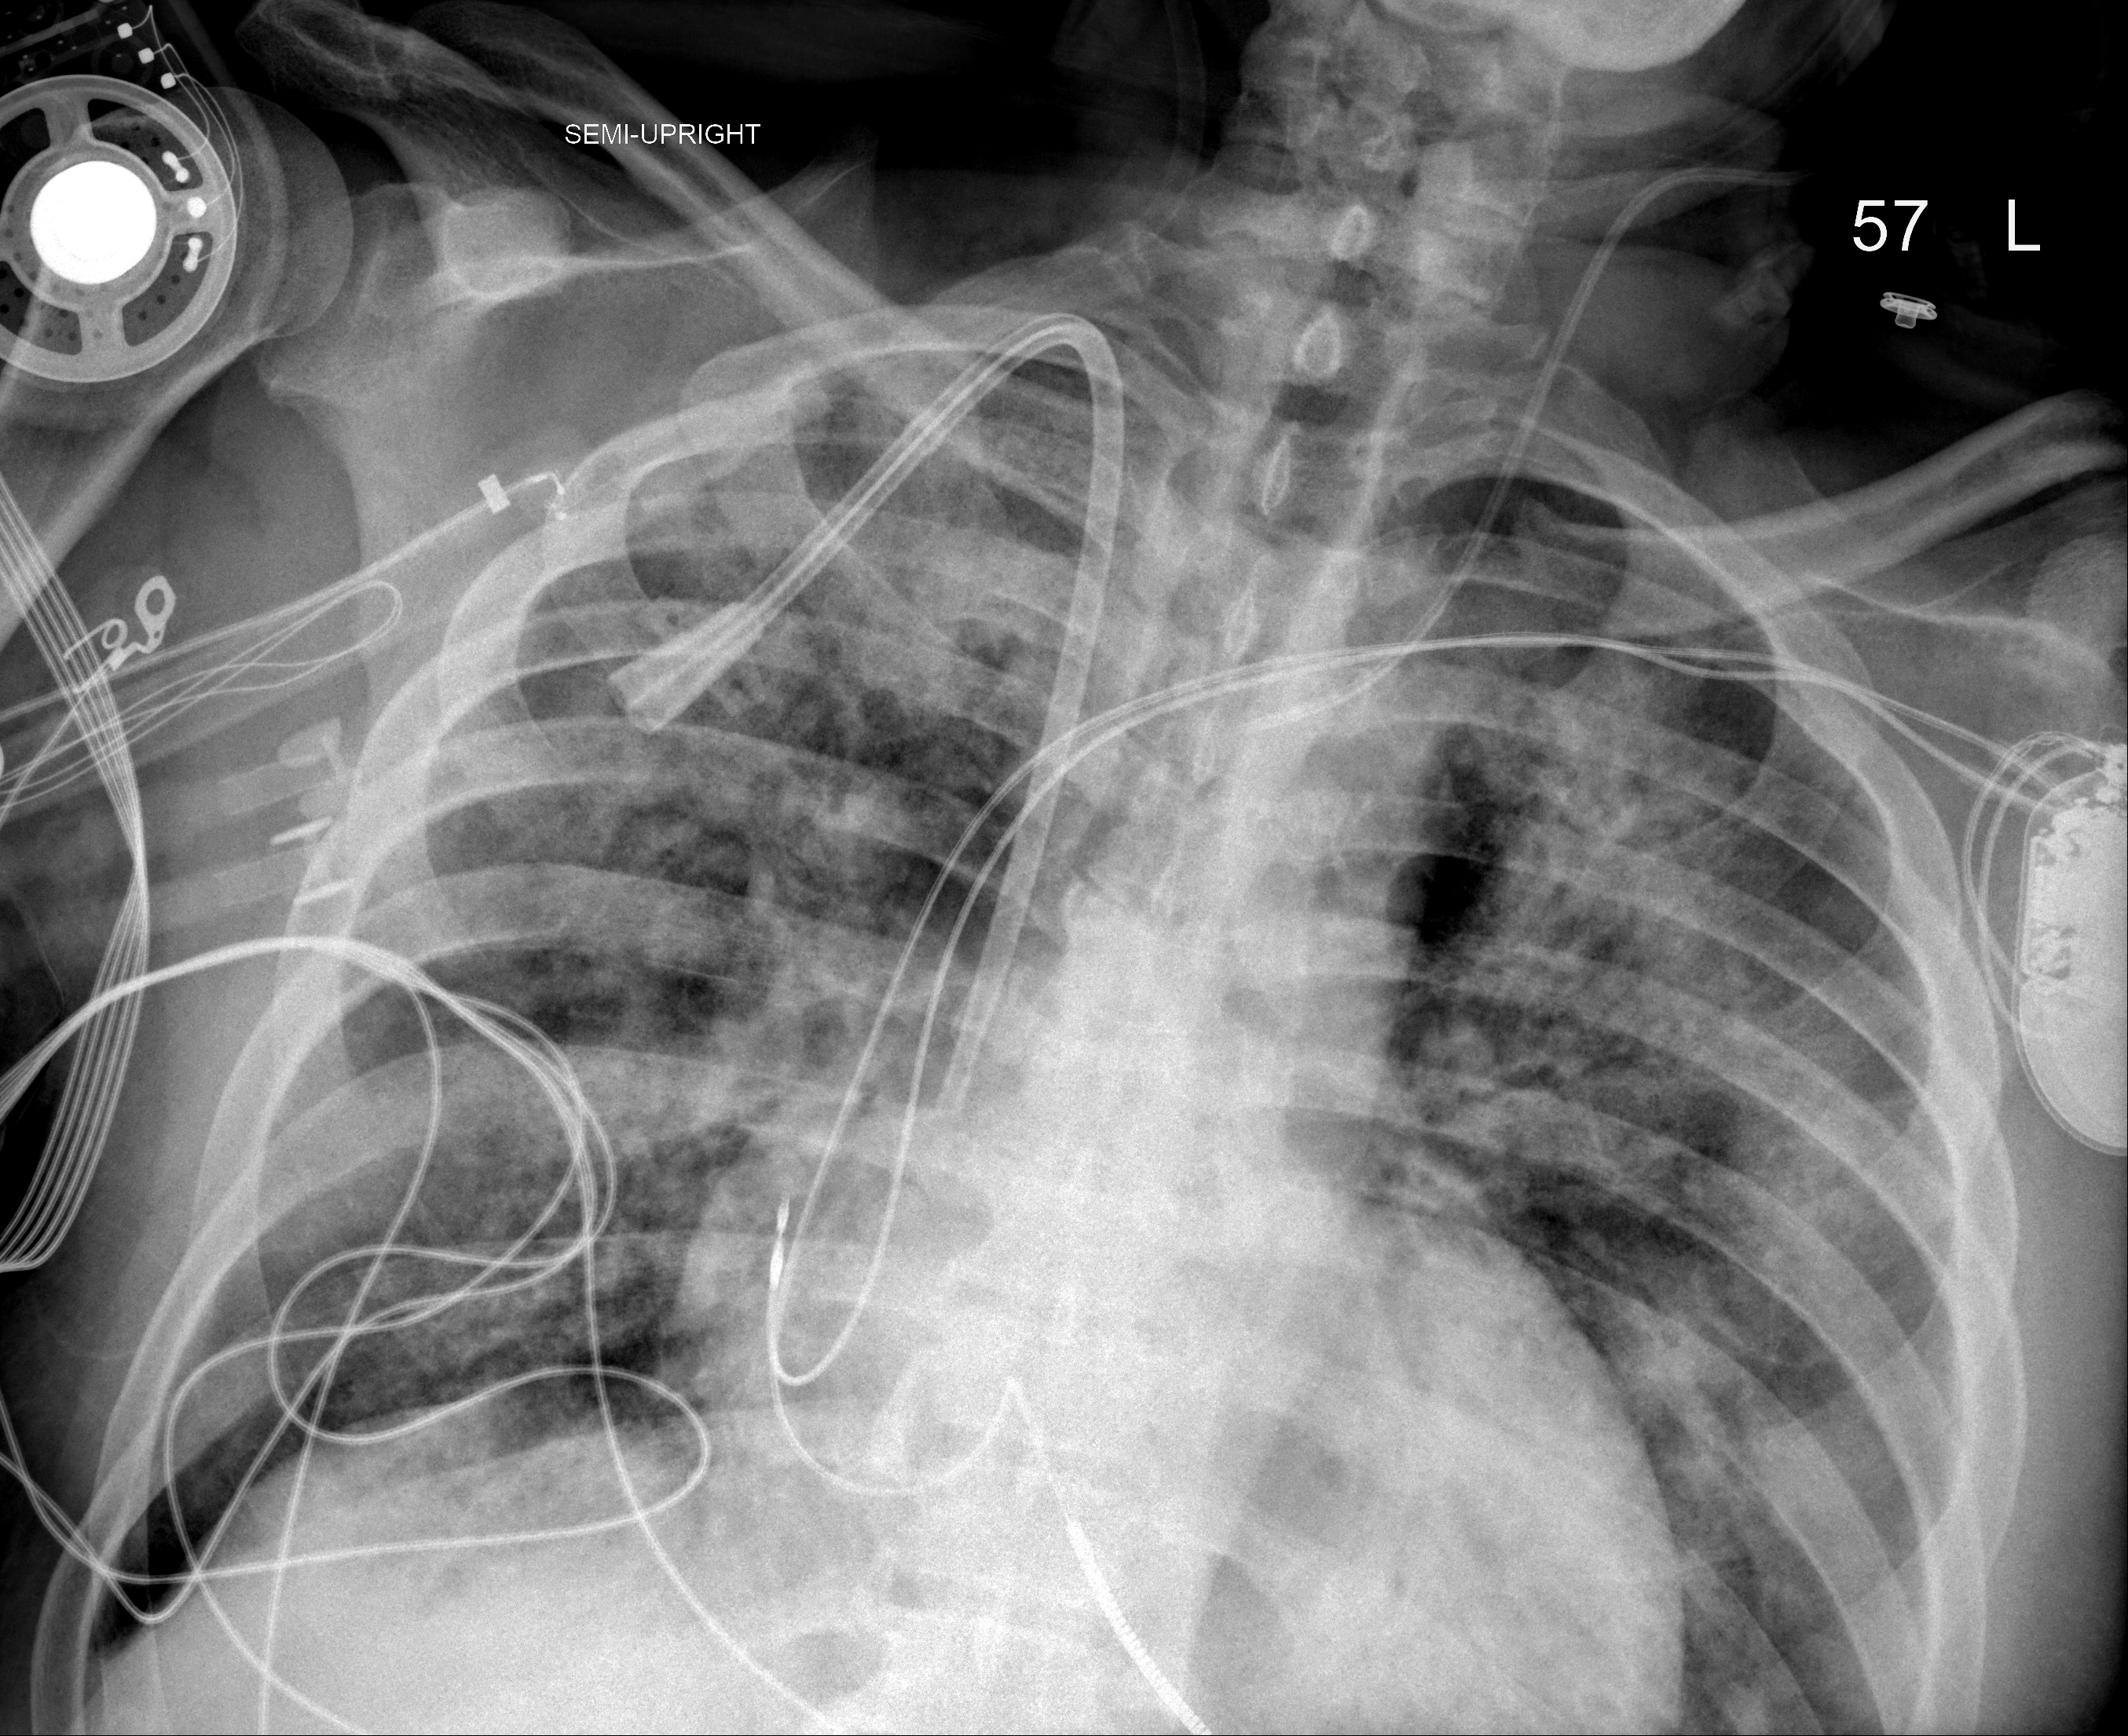
Portable chest radiograph, AP projection. Male patient, age 60 years; imaged 7 days after the COVID-19 diagnosis.
Key findings recorded by the radiologist: Little change in the diffuse bilateral airspace disease.